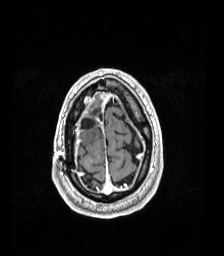
Brain MRI from a brain-tumour surgery series, one axial slice; T1-weighted post-contrast; 1 mm slice thickness; 224 × 256 image matrix, field of view 224 × 256 mm. Case-level facts recorded for this patient, not image findings: histopathology: Astrocytoma; WHO grade: 4.
Outlined on this slice (expert manual segmentation):
- previous resection cavity: box from (x=80, y=117) to (x=95, y=130) px